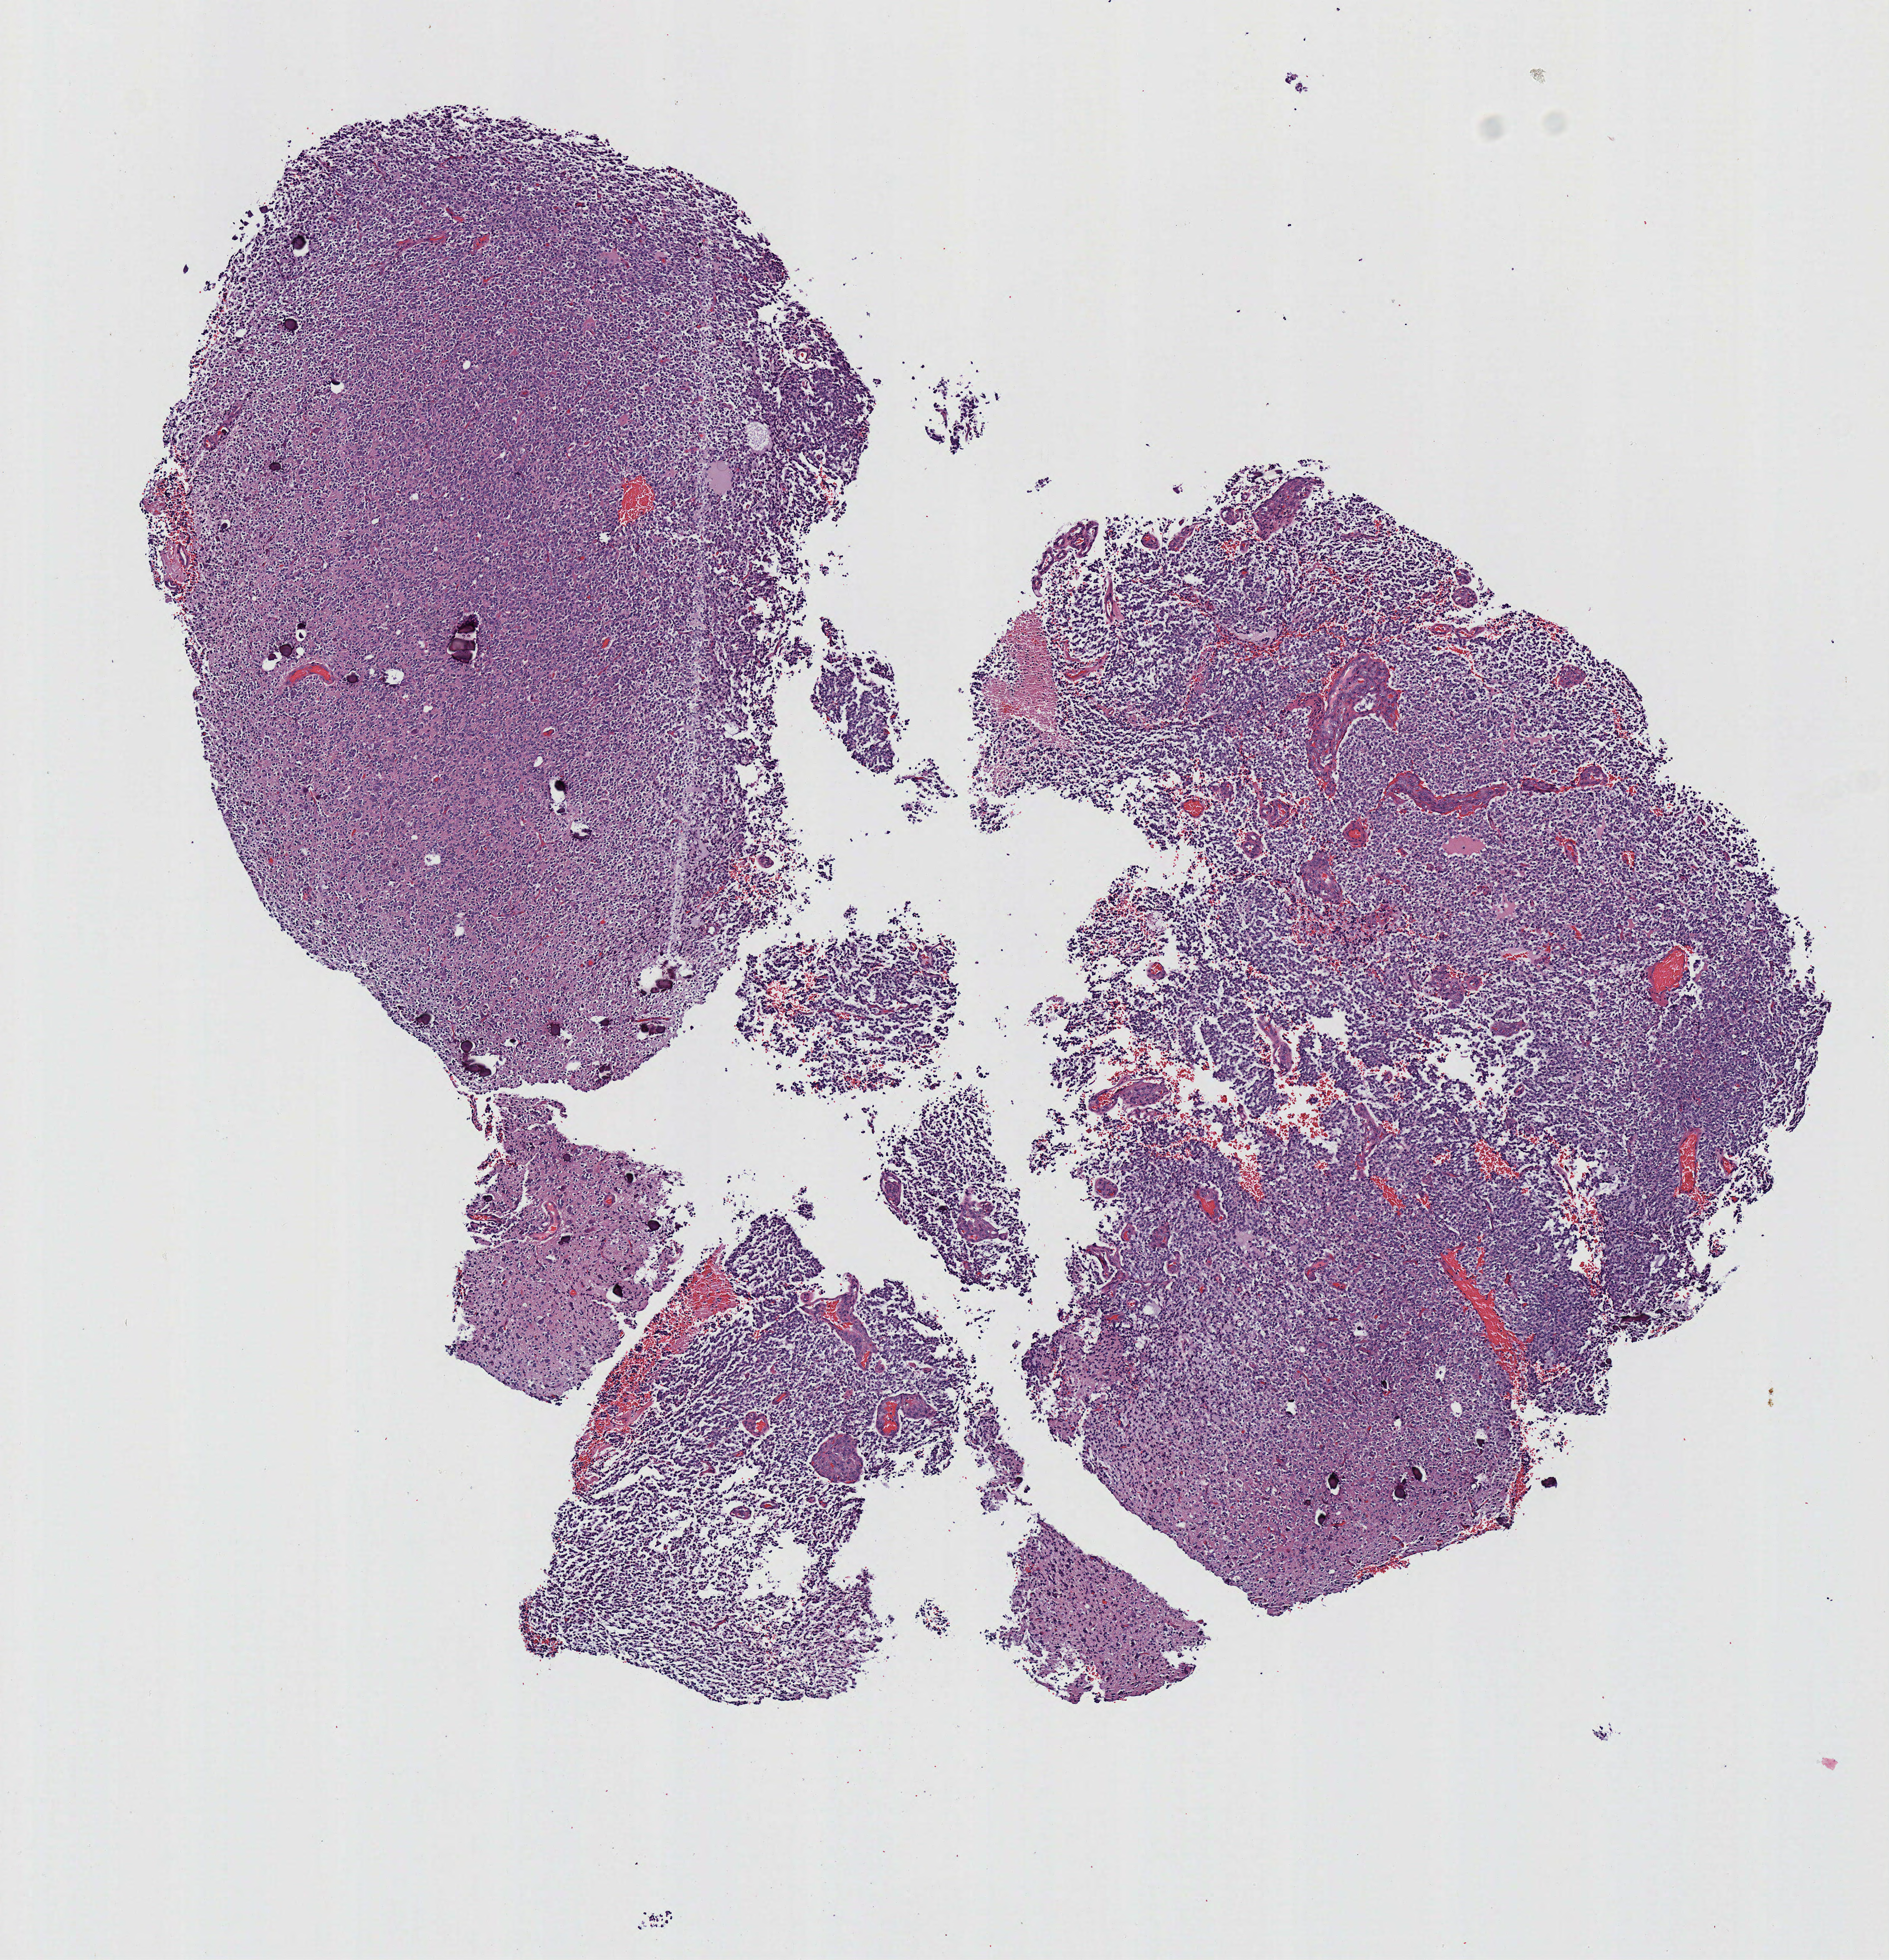
H&E whole-slide image, a low-resolution overview of the entire scanned area, about 5.9 x 6.1 mm (from a 40x scan). Frozen section from the top of the tissue portion. Brain, primary tumour sample. Male patient; age at initial diagnosis 56 years. Histologic grade: G3 (poorly differentiated). Slide review estimates, as recorded: tumour cells 100%, tumour nuclei 85%, normal cells 0%, stromal cells 0%, necrosis 0%.
Pathologic diagnosis: Oligodendroglioma, anaplastic. Laterality: midline.